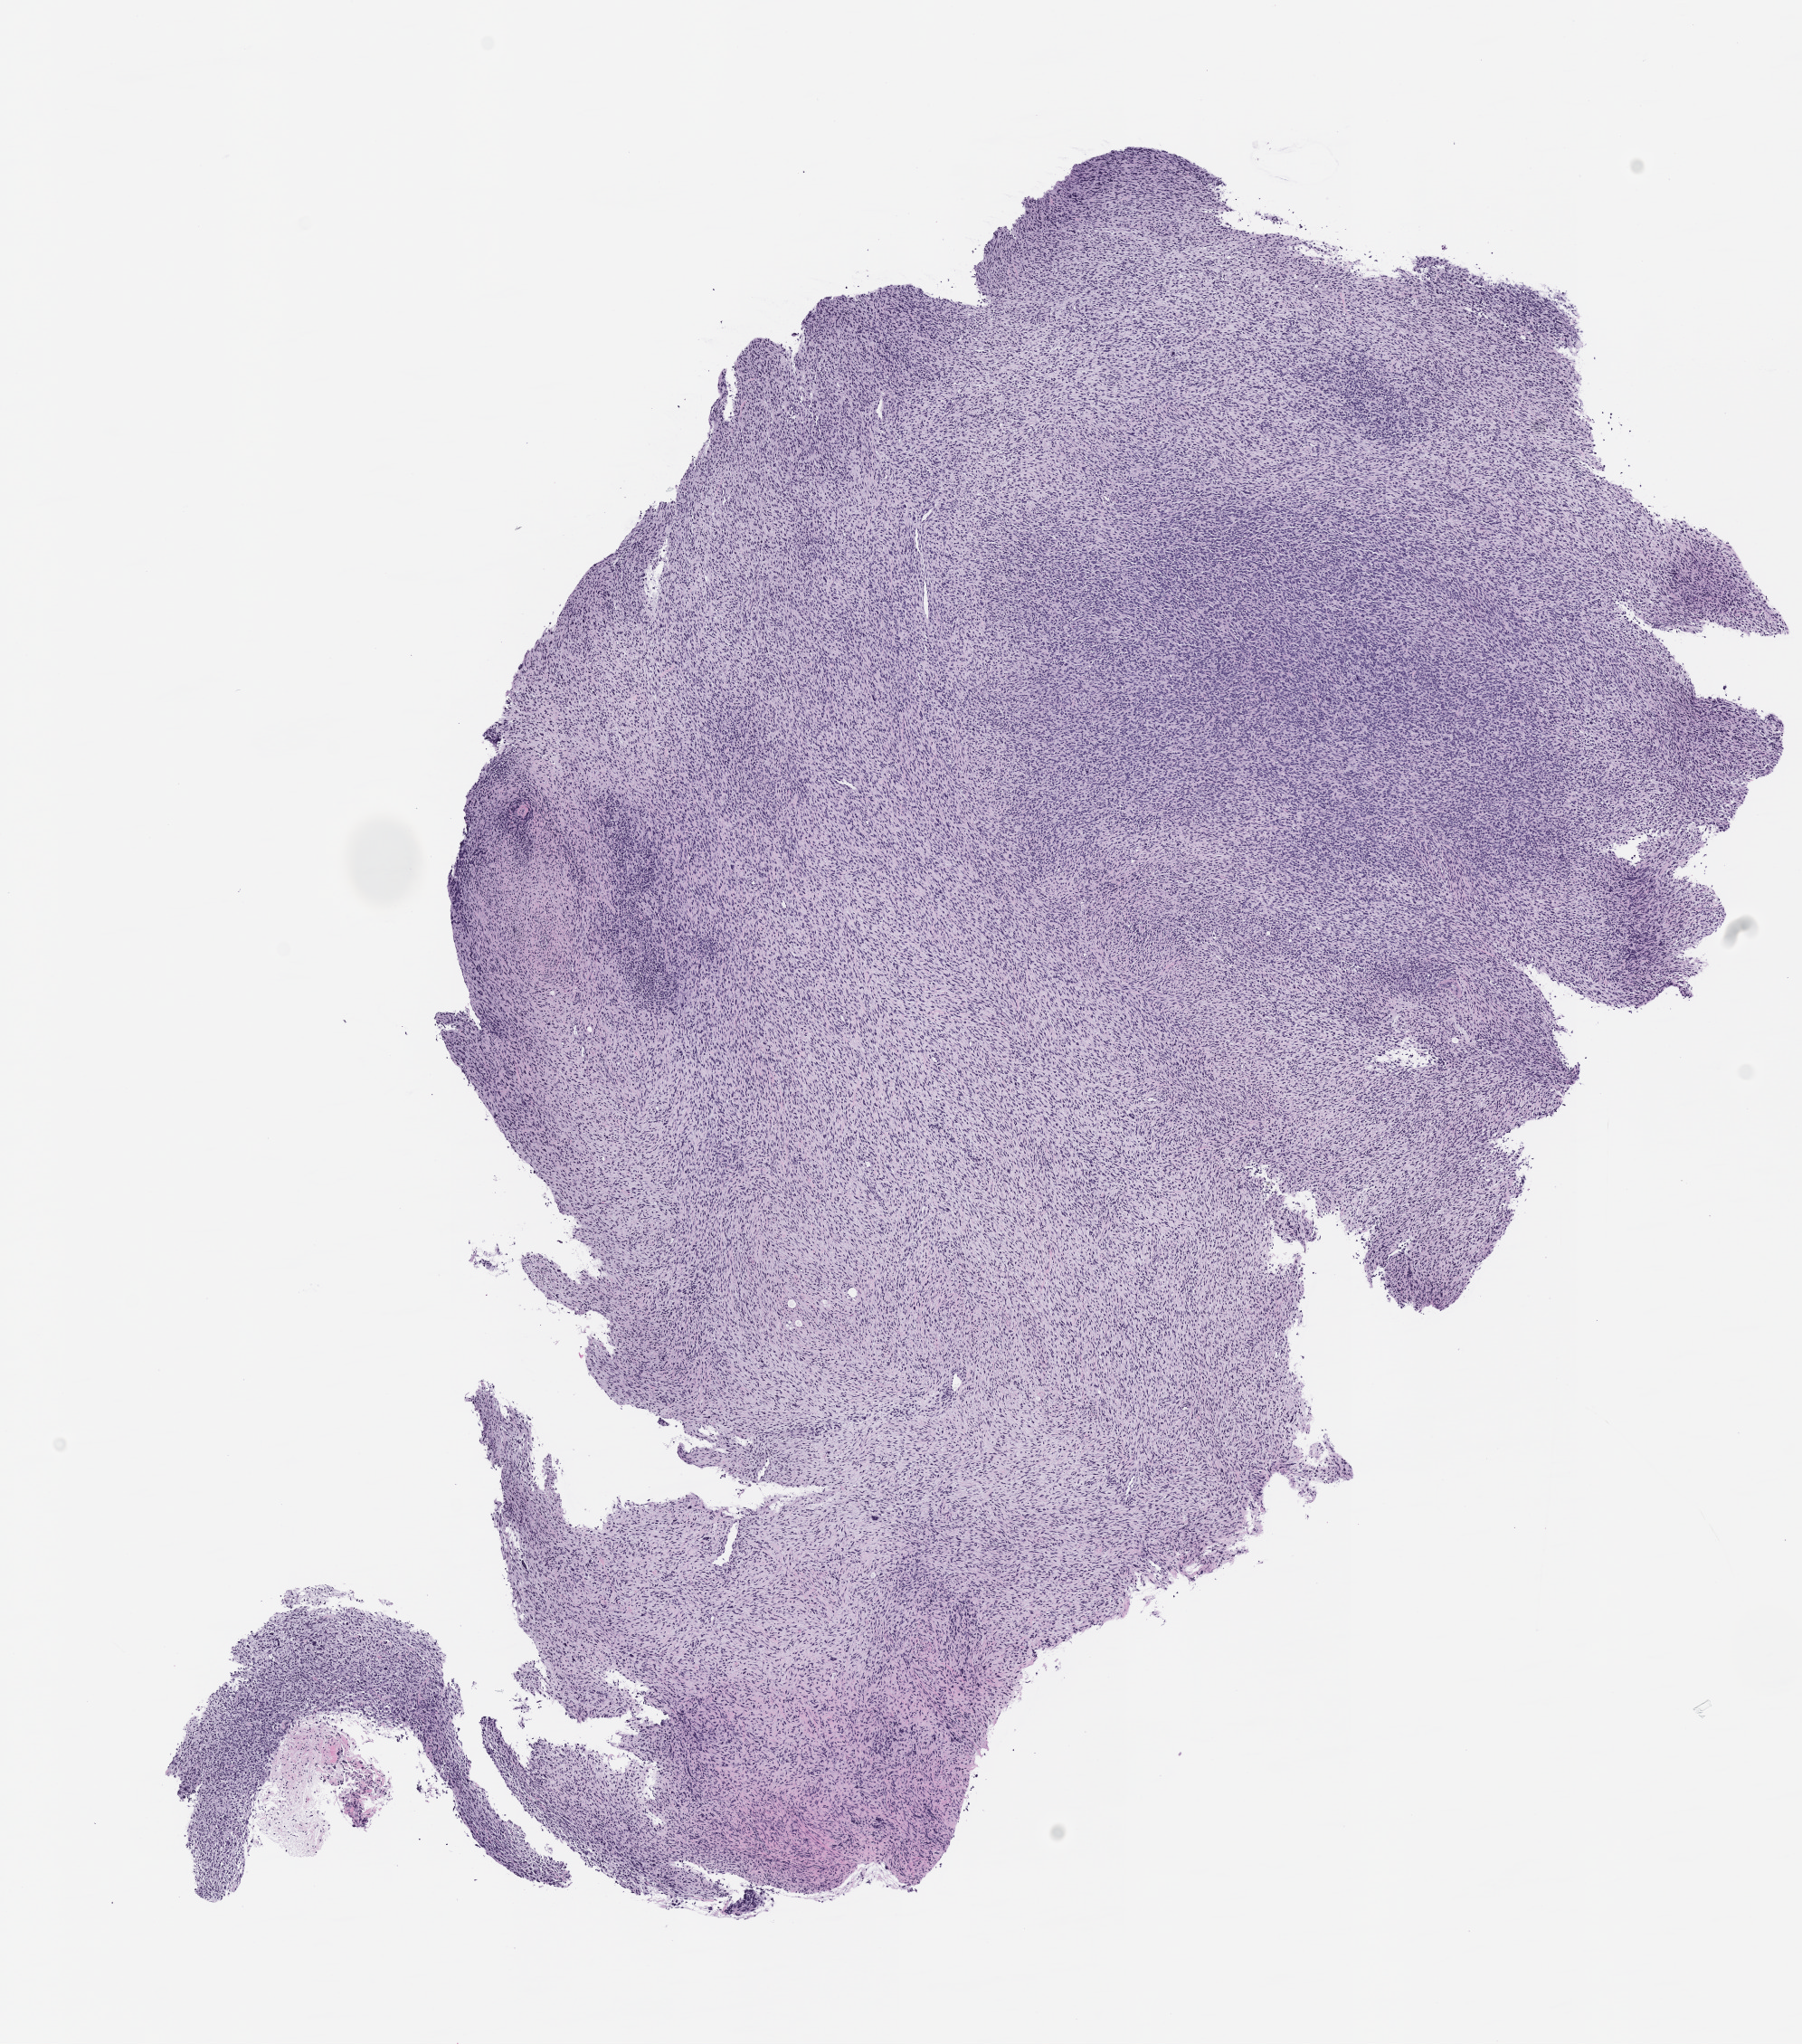
Hematoxylin and eosin (H&E) whole-slide image of a patient-derived xenograft (PDX) tumor grown in a mouse, passage 1 — shown as a low-resolution overview of the whole scanned area (about 8.0 x 9.1 mm), FFPE section, tumor site category: peripheral nervous system.
Originating patient diagnosis: Malignant Peripheral Nerve Sheath Tumor.